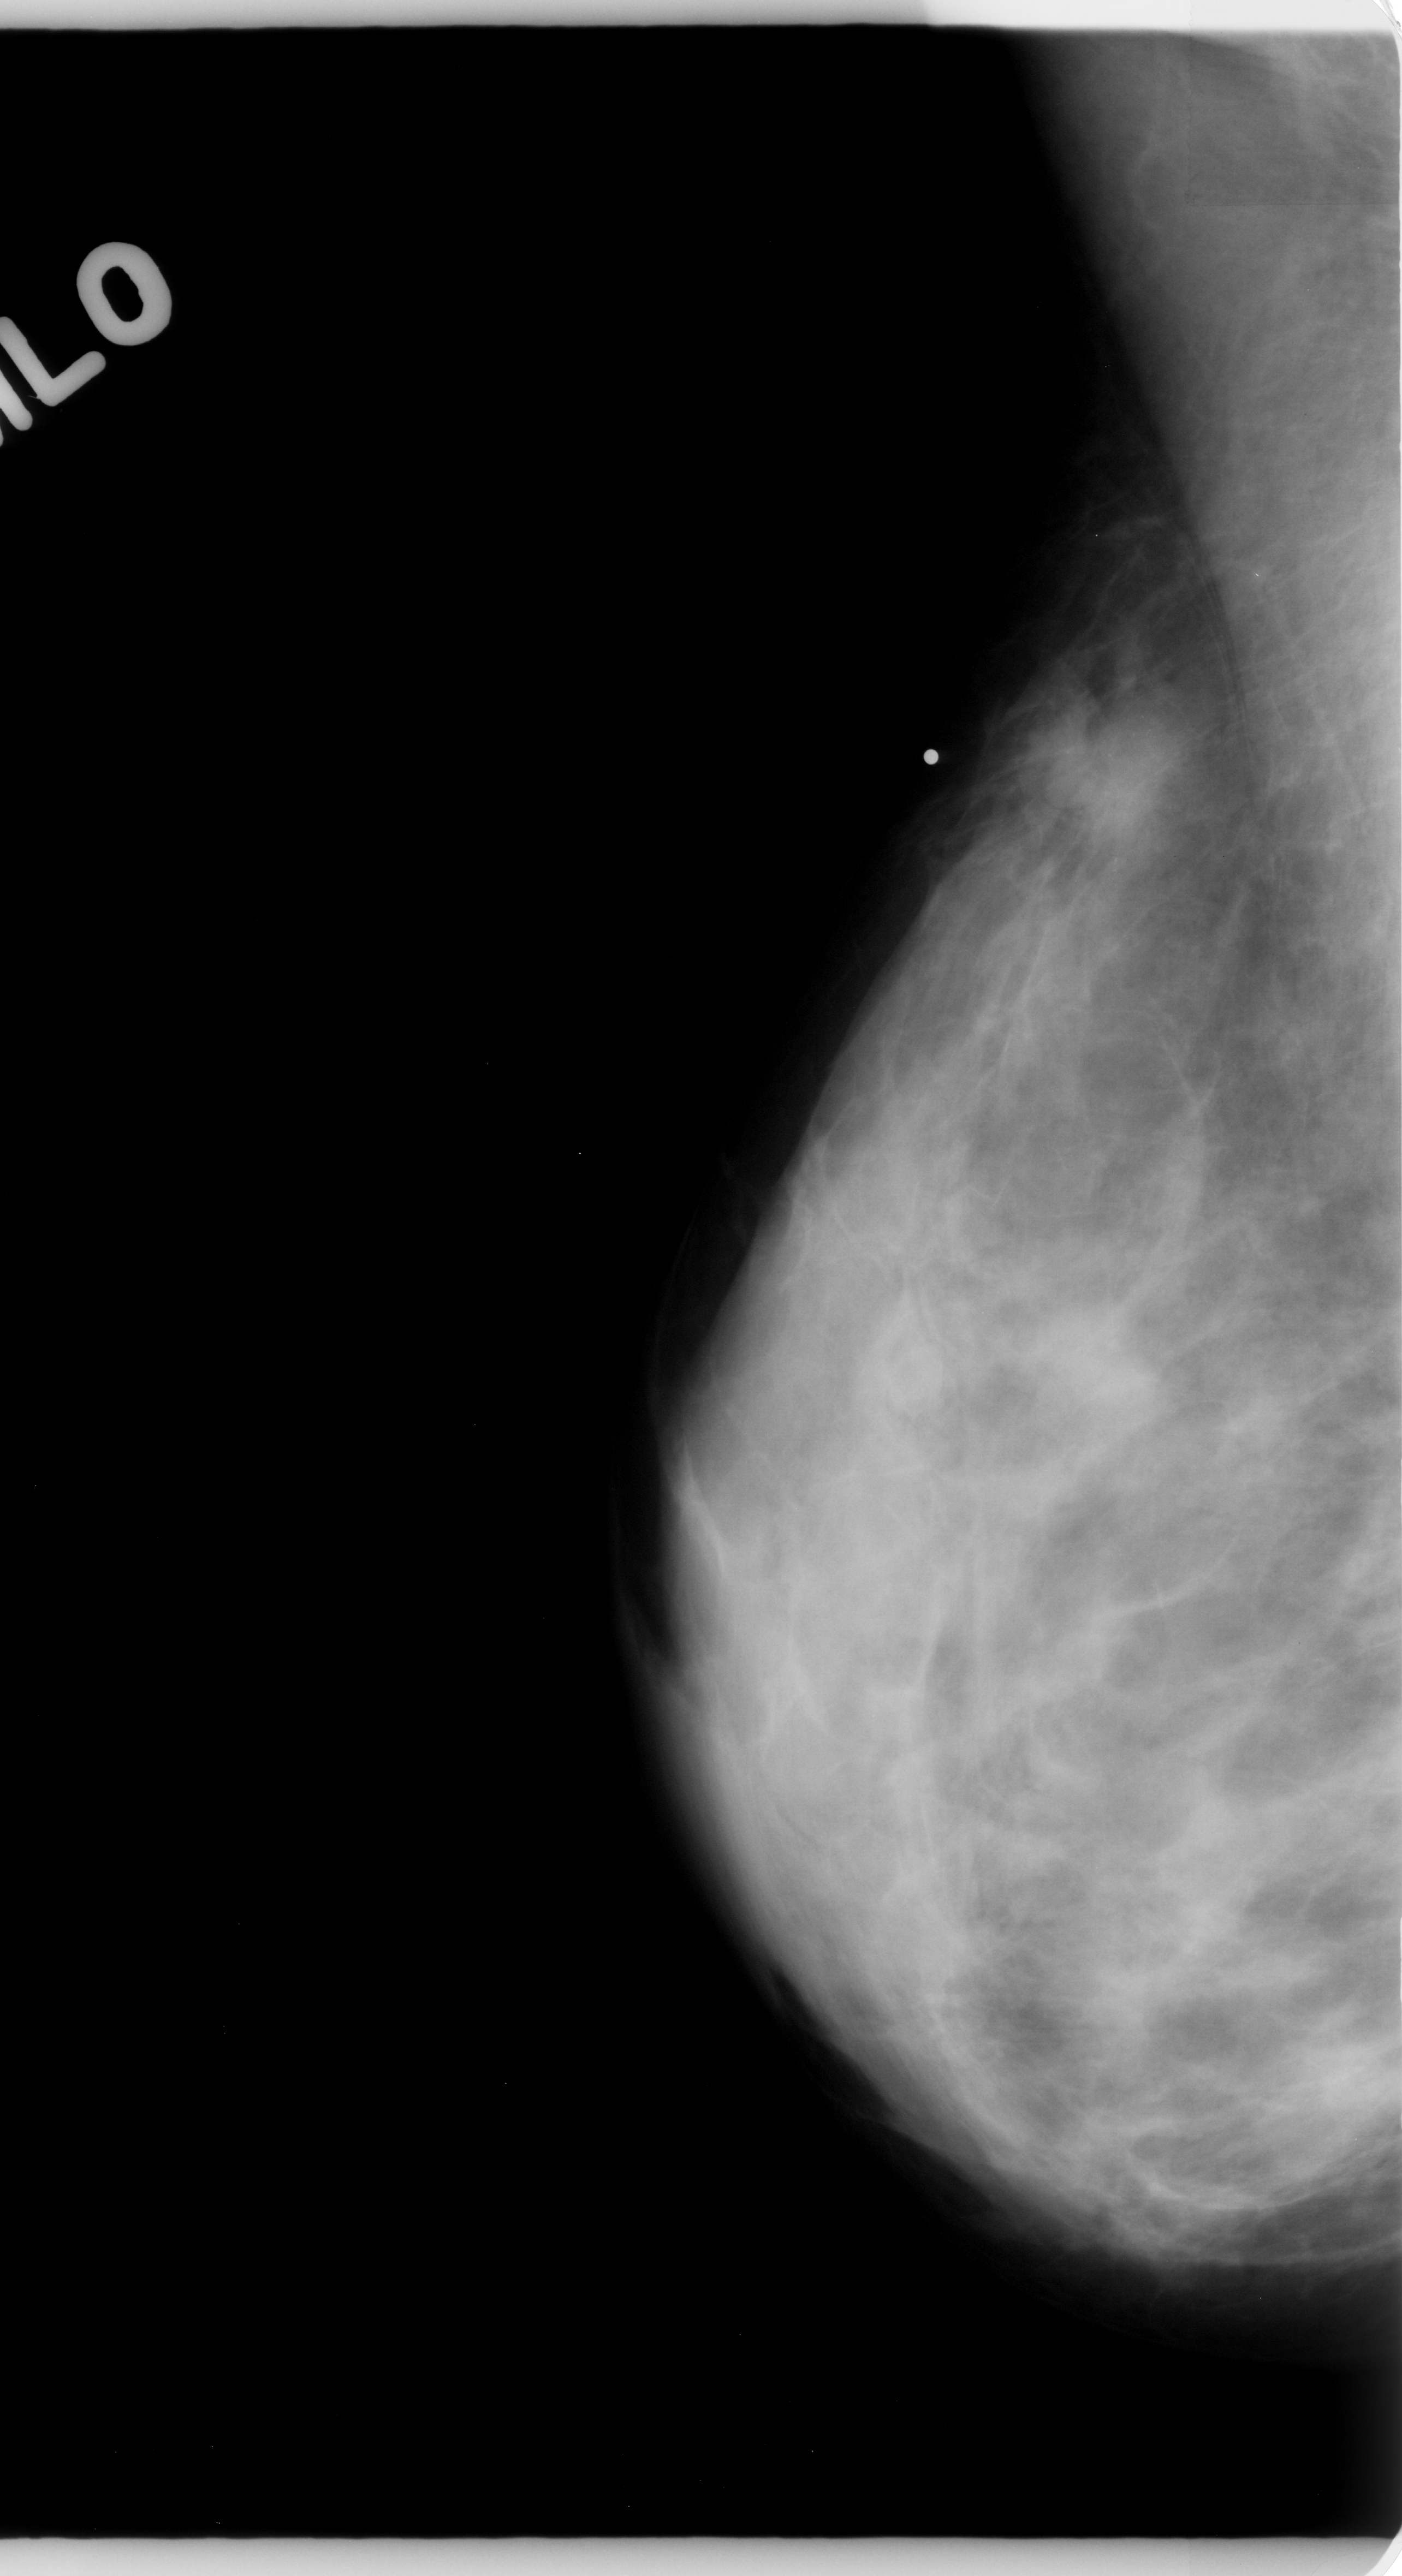
Digitized screen-film mammogram; right breast; mediolateral oblique (MLO) view; 1402 × 2576 image matrix.
Expert-marked regions of interest on this film, with their recorded descriptors:
- mass, shape irregular, margins spiculated; BI-RADS assessment category 5; subtlety rating 4 on a 1 (subtle) to 5 (obvious) scale; pathology result (as recorded, not read from the image): malignant: bounding box (x1, y1, x2, y2) in pixels: (1008, 674, 1198, 920)